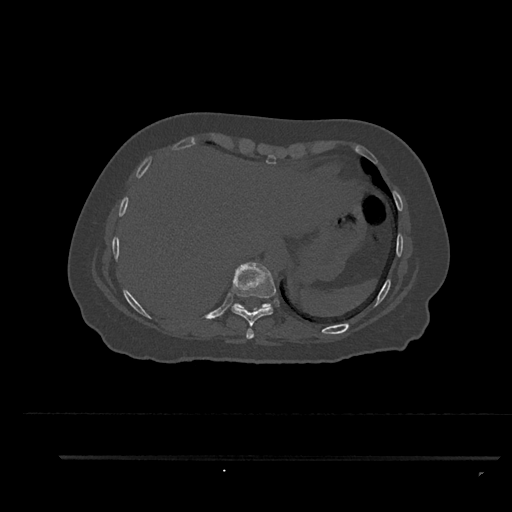
CT including the spine, one axial slice; slice 403 of 797 in the series (ordered by position); bone window (W 1800 / L 400 HU); 0.5 mm slice thickness; 512 × 512 image matrix, field of view 408 × 408 mm. Patient: female, 44 years. From the clinical record (not read from this slice): primary cancer: renal.
Annotated regions visible in this slice (semi-automatic segmentation, software-assisted and operator-edited):
- T10 vertebra: bounding box [x1, y1, x2, y2] px = [233, 303, 272, 308]
- T8 vertebra: [246, 328, 254, 339]
- T9 vertebra: [231, 262, 276, 327]